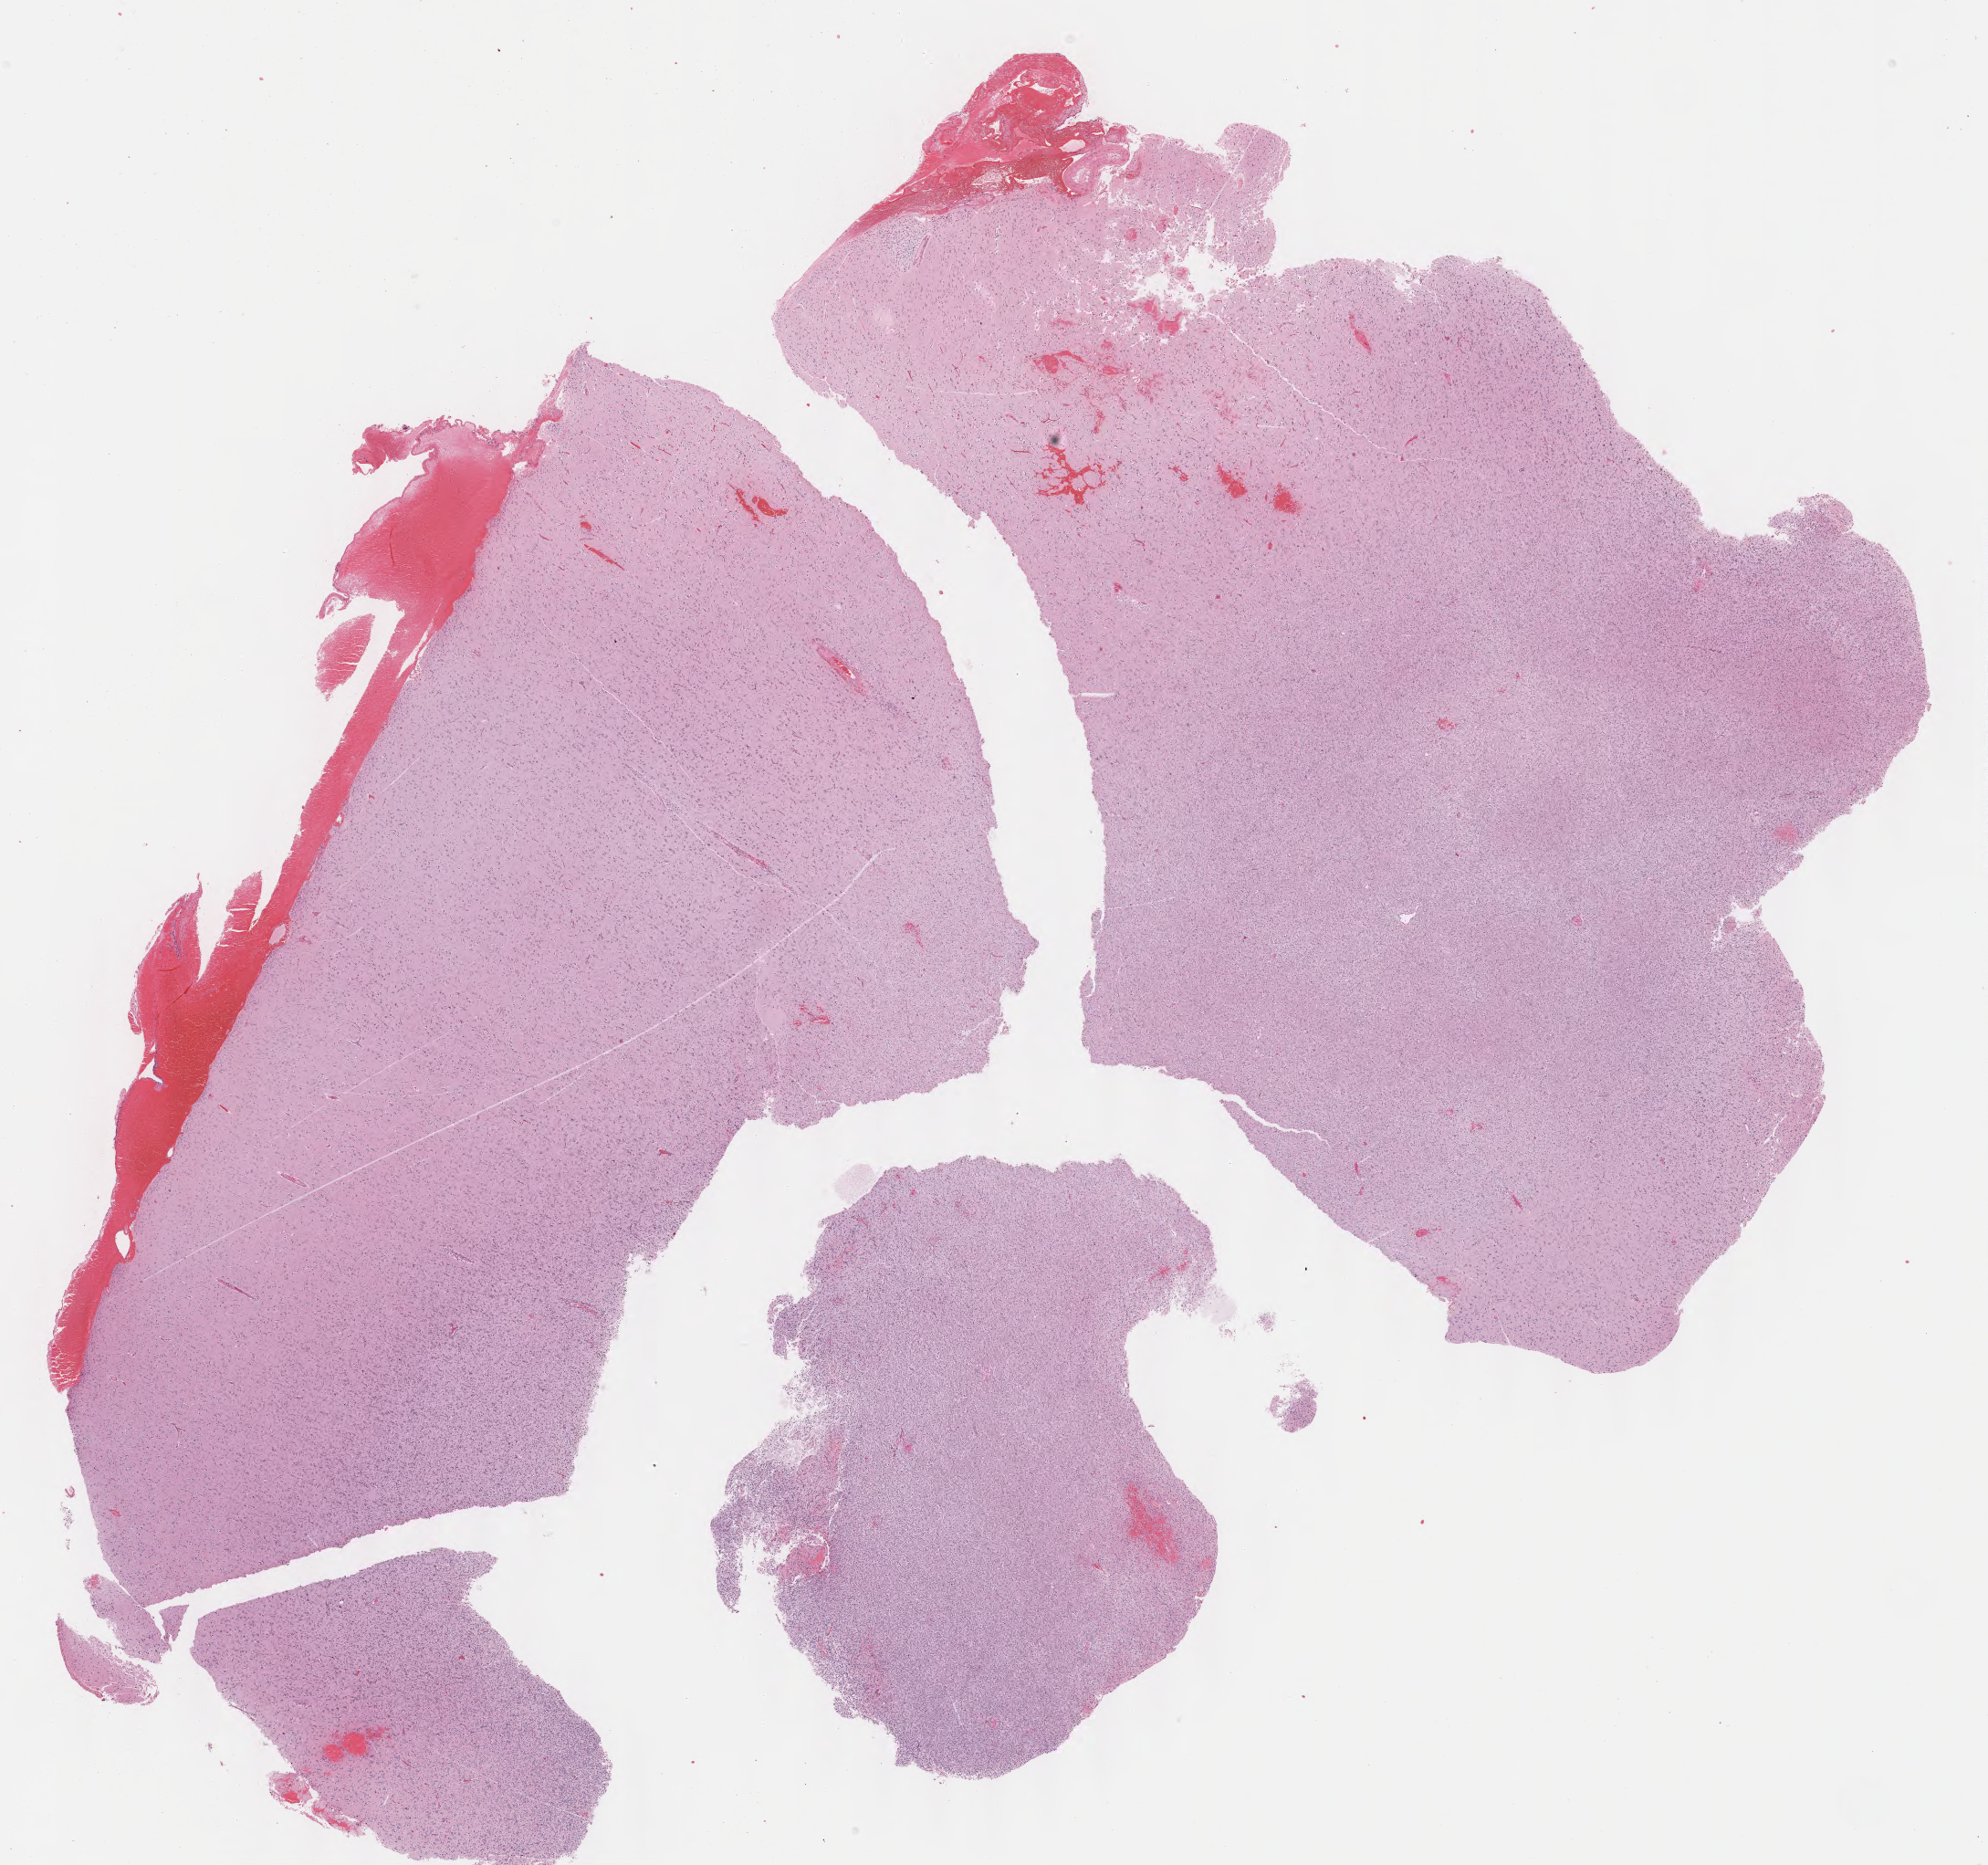
Whole-slide histology image, Hematoxylin and eosin (H&E) stained, a low-resolution overview of the entire scanned area, about 17.2 x 16.2 mm. Formalin-fixed paraffin-embedded (FFPE) diagnostic section. Primary tumour sample from the brain. Female, age 65 years at initial diagnosis. Histologic grade: G3 (poorly differentiated).
Laterality: right. Diagnosis: Mixed glioma.